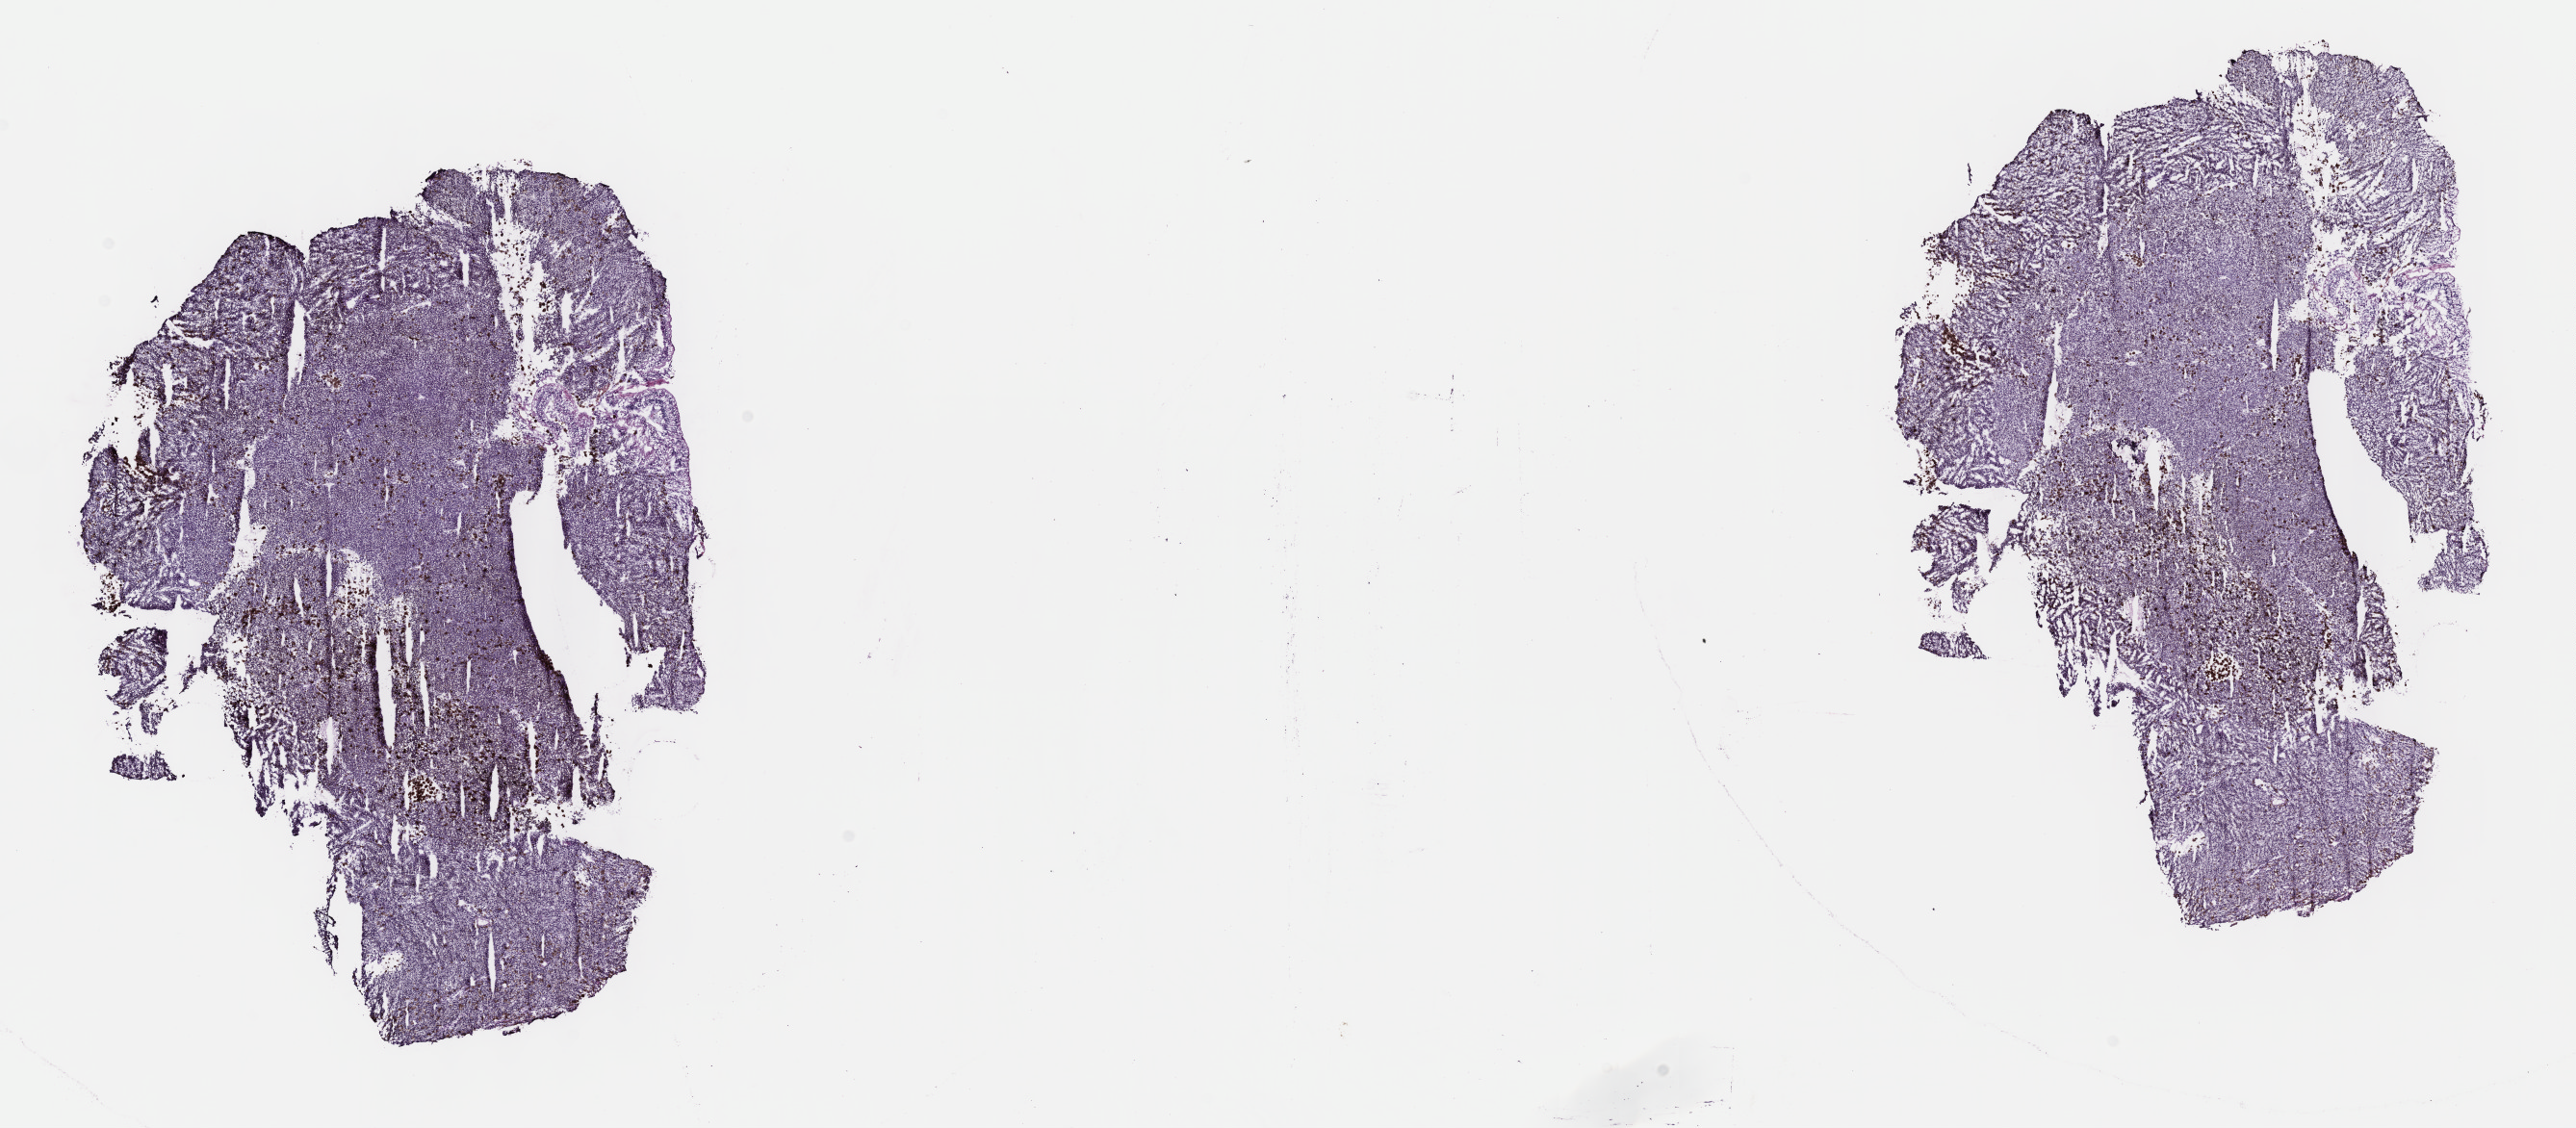
Whole-slide histology image, Hematoxylin and eosin (H&E) stained, whole scanned area (about 21.6 x 9.5 mm, slide scanned at 40x) shown as a low-resolution overview, frozen section, primary tumour sample from the uvea. Female, age 79 years at initial diagnosis. Slide review estimates, as recorded: tumour cells 100%, tumour nuclei 80%, normal cells 0%, stromal cells 0%, necrosis 0%. Infiltration values recorded for this section: lymphocyte infiltration 2%, monocyte infiltration 0%, neutrophil infiltration 0%.
• AJCC pathologic stage: IIIB
• pathologic diagnosis: Spindle cell melanoma, NOS (eye, NOS)